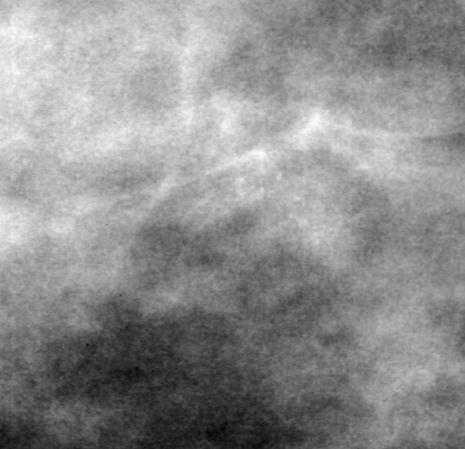
Crop from a digitized film mammogram around one marked abnormality; left breast; CC view.
Marked abnormality: calcifications, morphology pleomorphic, distribution clustered; BI-RADS assessment category 4; pathology result (as recorded, not read from the image): benign.